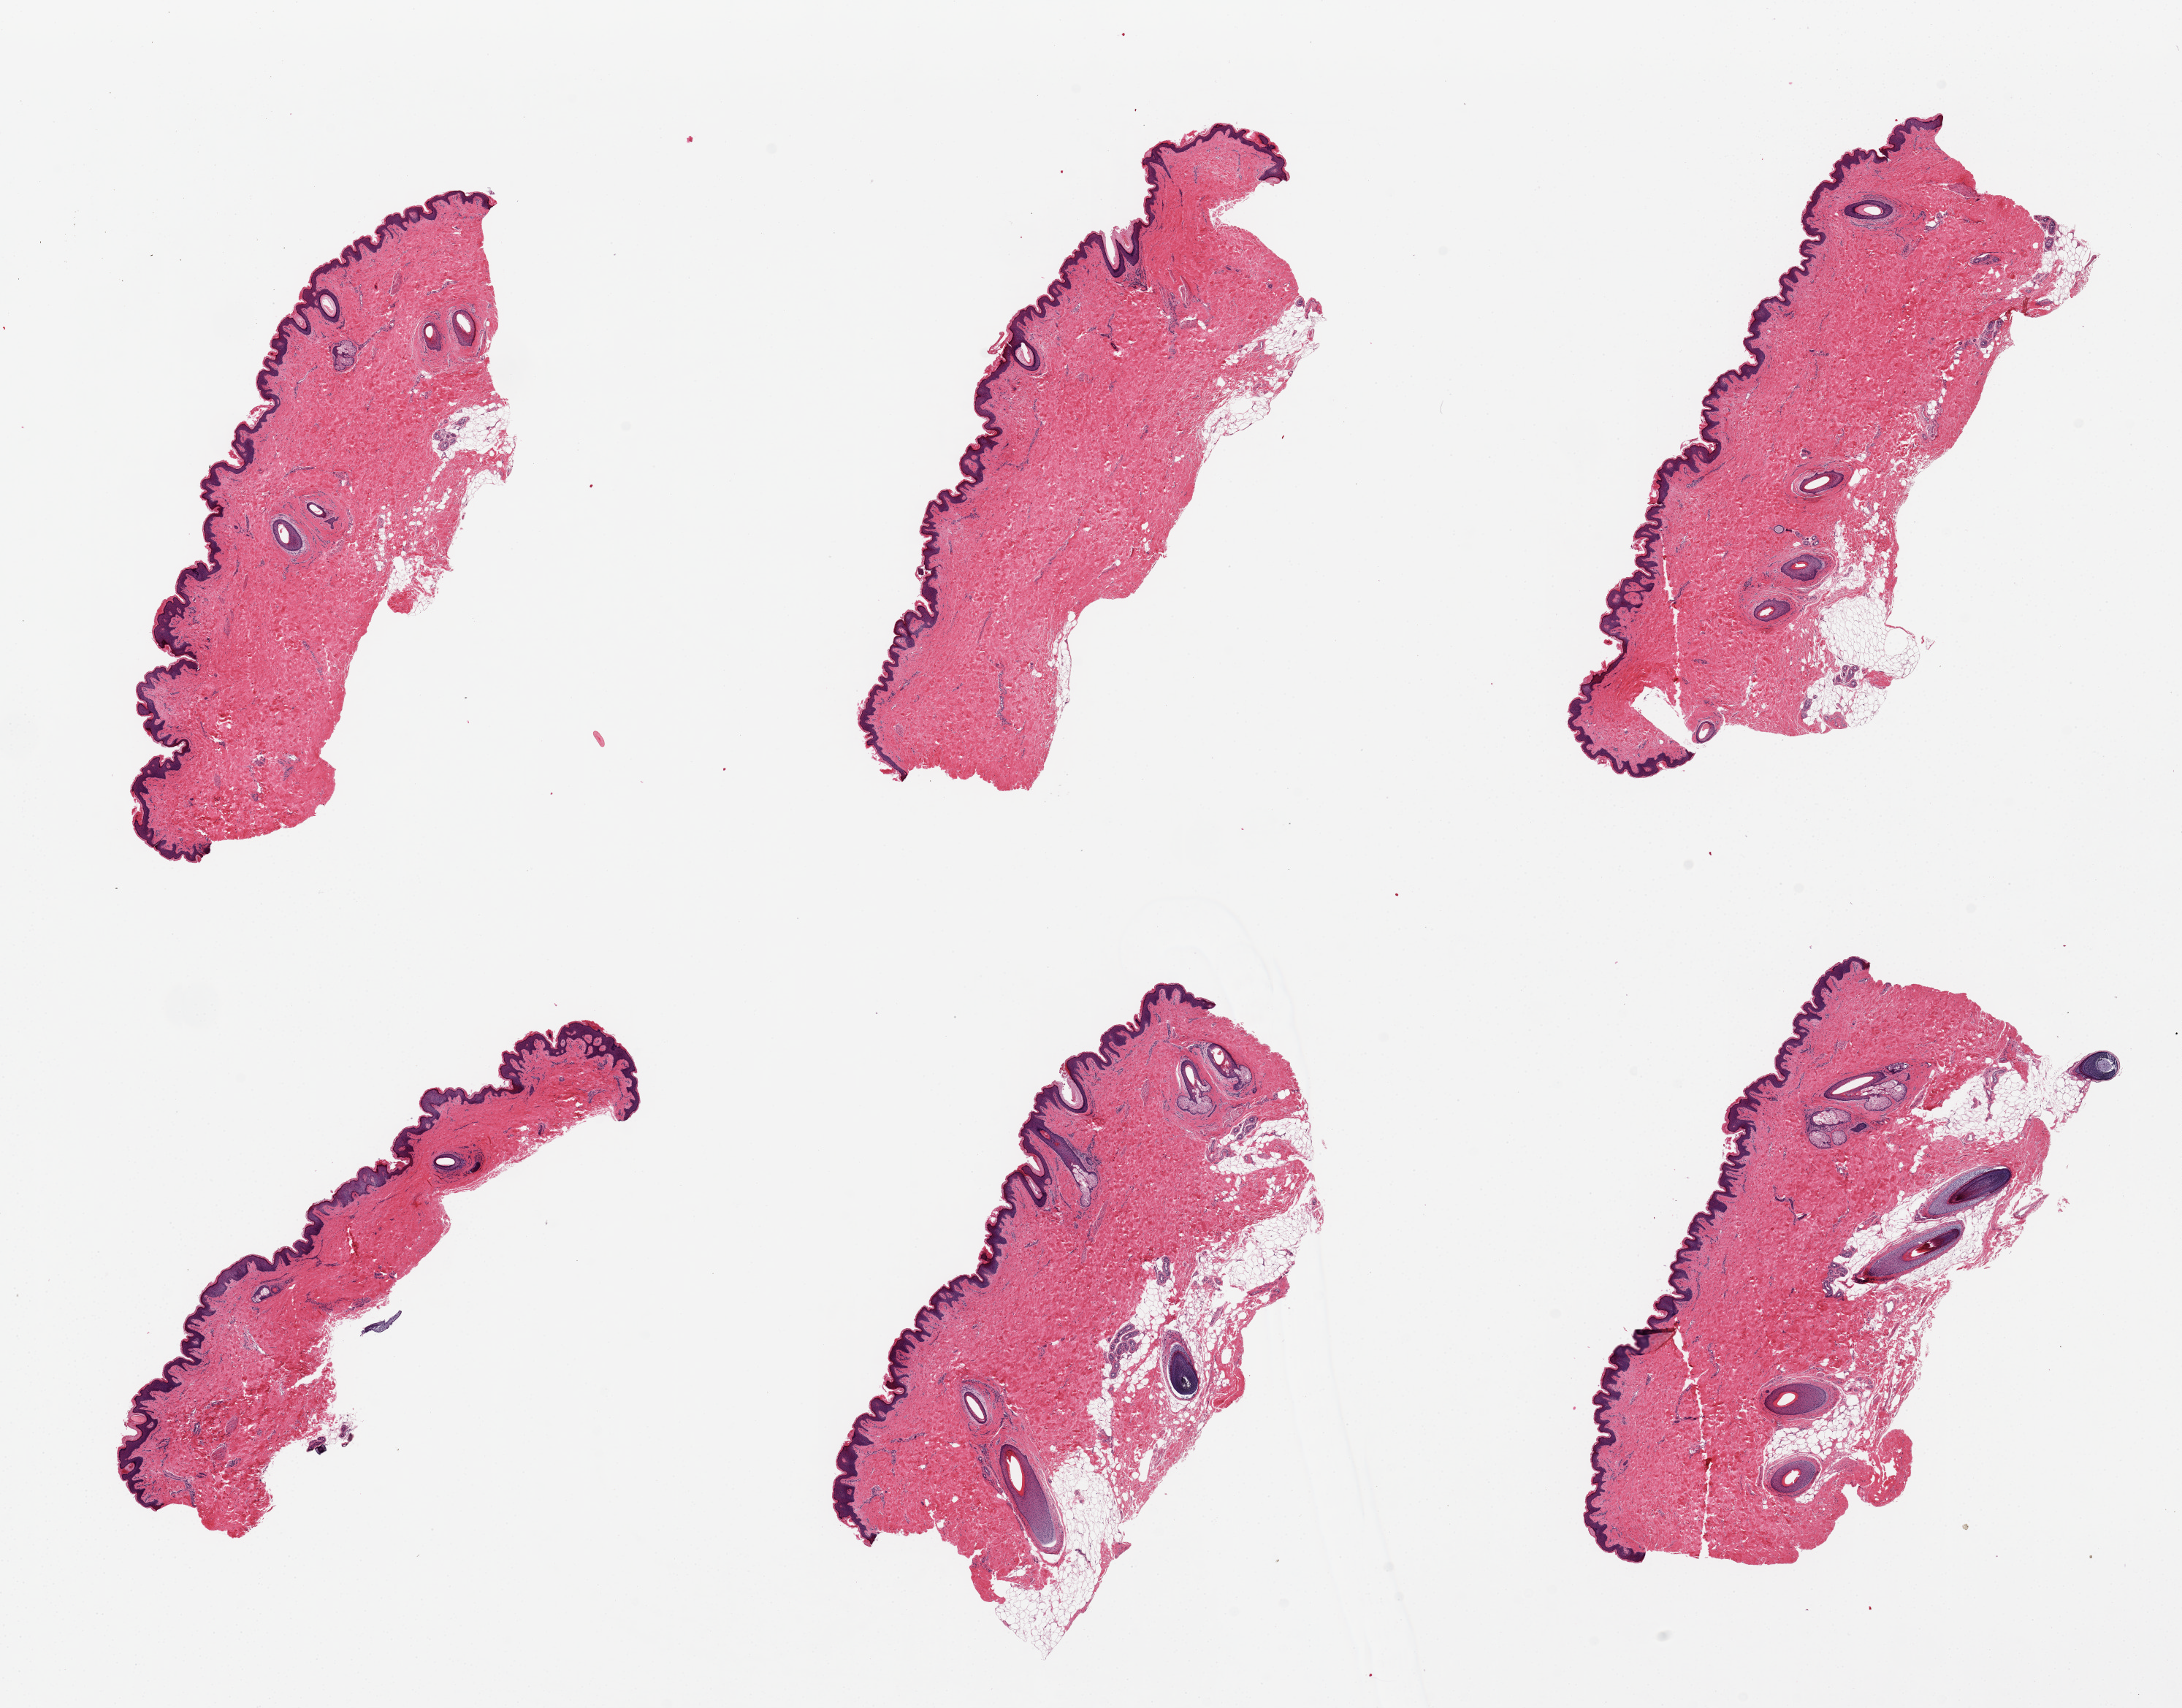
Digitized H&E-stained section, low-resolution overview of the scanned area, about 23.6 x 18.5 mm (slide scanned at 20x); PAXgene-fixed, paraffin-embedded tissue; target tissue: skin of suprapubic region; tissue donor sample. Female donor.
Reviewer comment on this tissue sample: 6 pieces; minimal adherent subcutaneous fat; squamous epithelium is ~50-60microns thick.